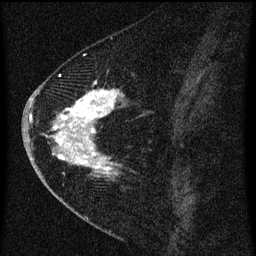
Breast MRI (dynamic contrast-enhanced), one sagittal slice. Slice 27 of 60 in the series (ordered by position). Dynamic contrast-enhanced series, image 2 of 3 at this slice position (ordered by acquisition). 1.5 T. TE 4.2 ms, TR 8 ms. 2 mm slice thickness. 256 × 256 image matrix. Female patient, age 47 years.
Annotated regions visible in this slice (semi-automatic segmentation, software-assisted and operator-edited):
- analysis volume of interest (the breast-tissue region the enhancement analysis was run in; not a lesion): bounding box [x1, y1, x2, y2] px = [38, 76, 137, 193]
- tumour enhancement mask (voxels above the 70 % enhancement threshold inside the analysis volume of interest): [46, 76, 123, 177]